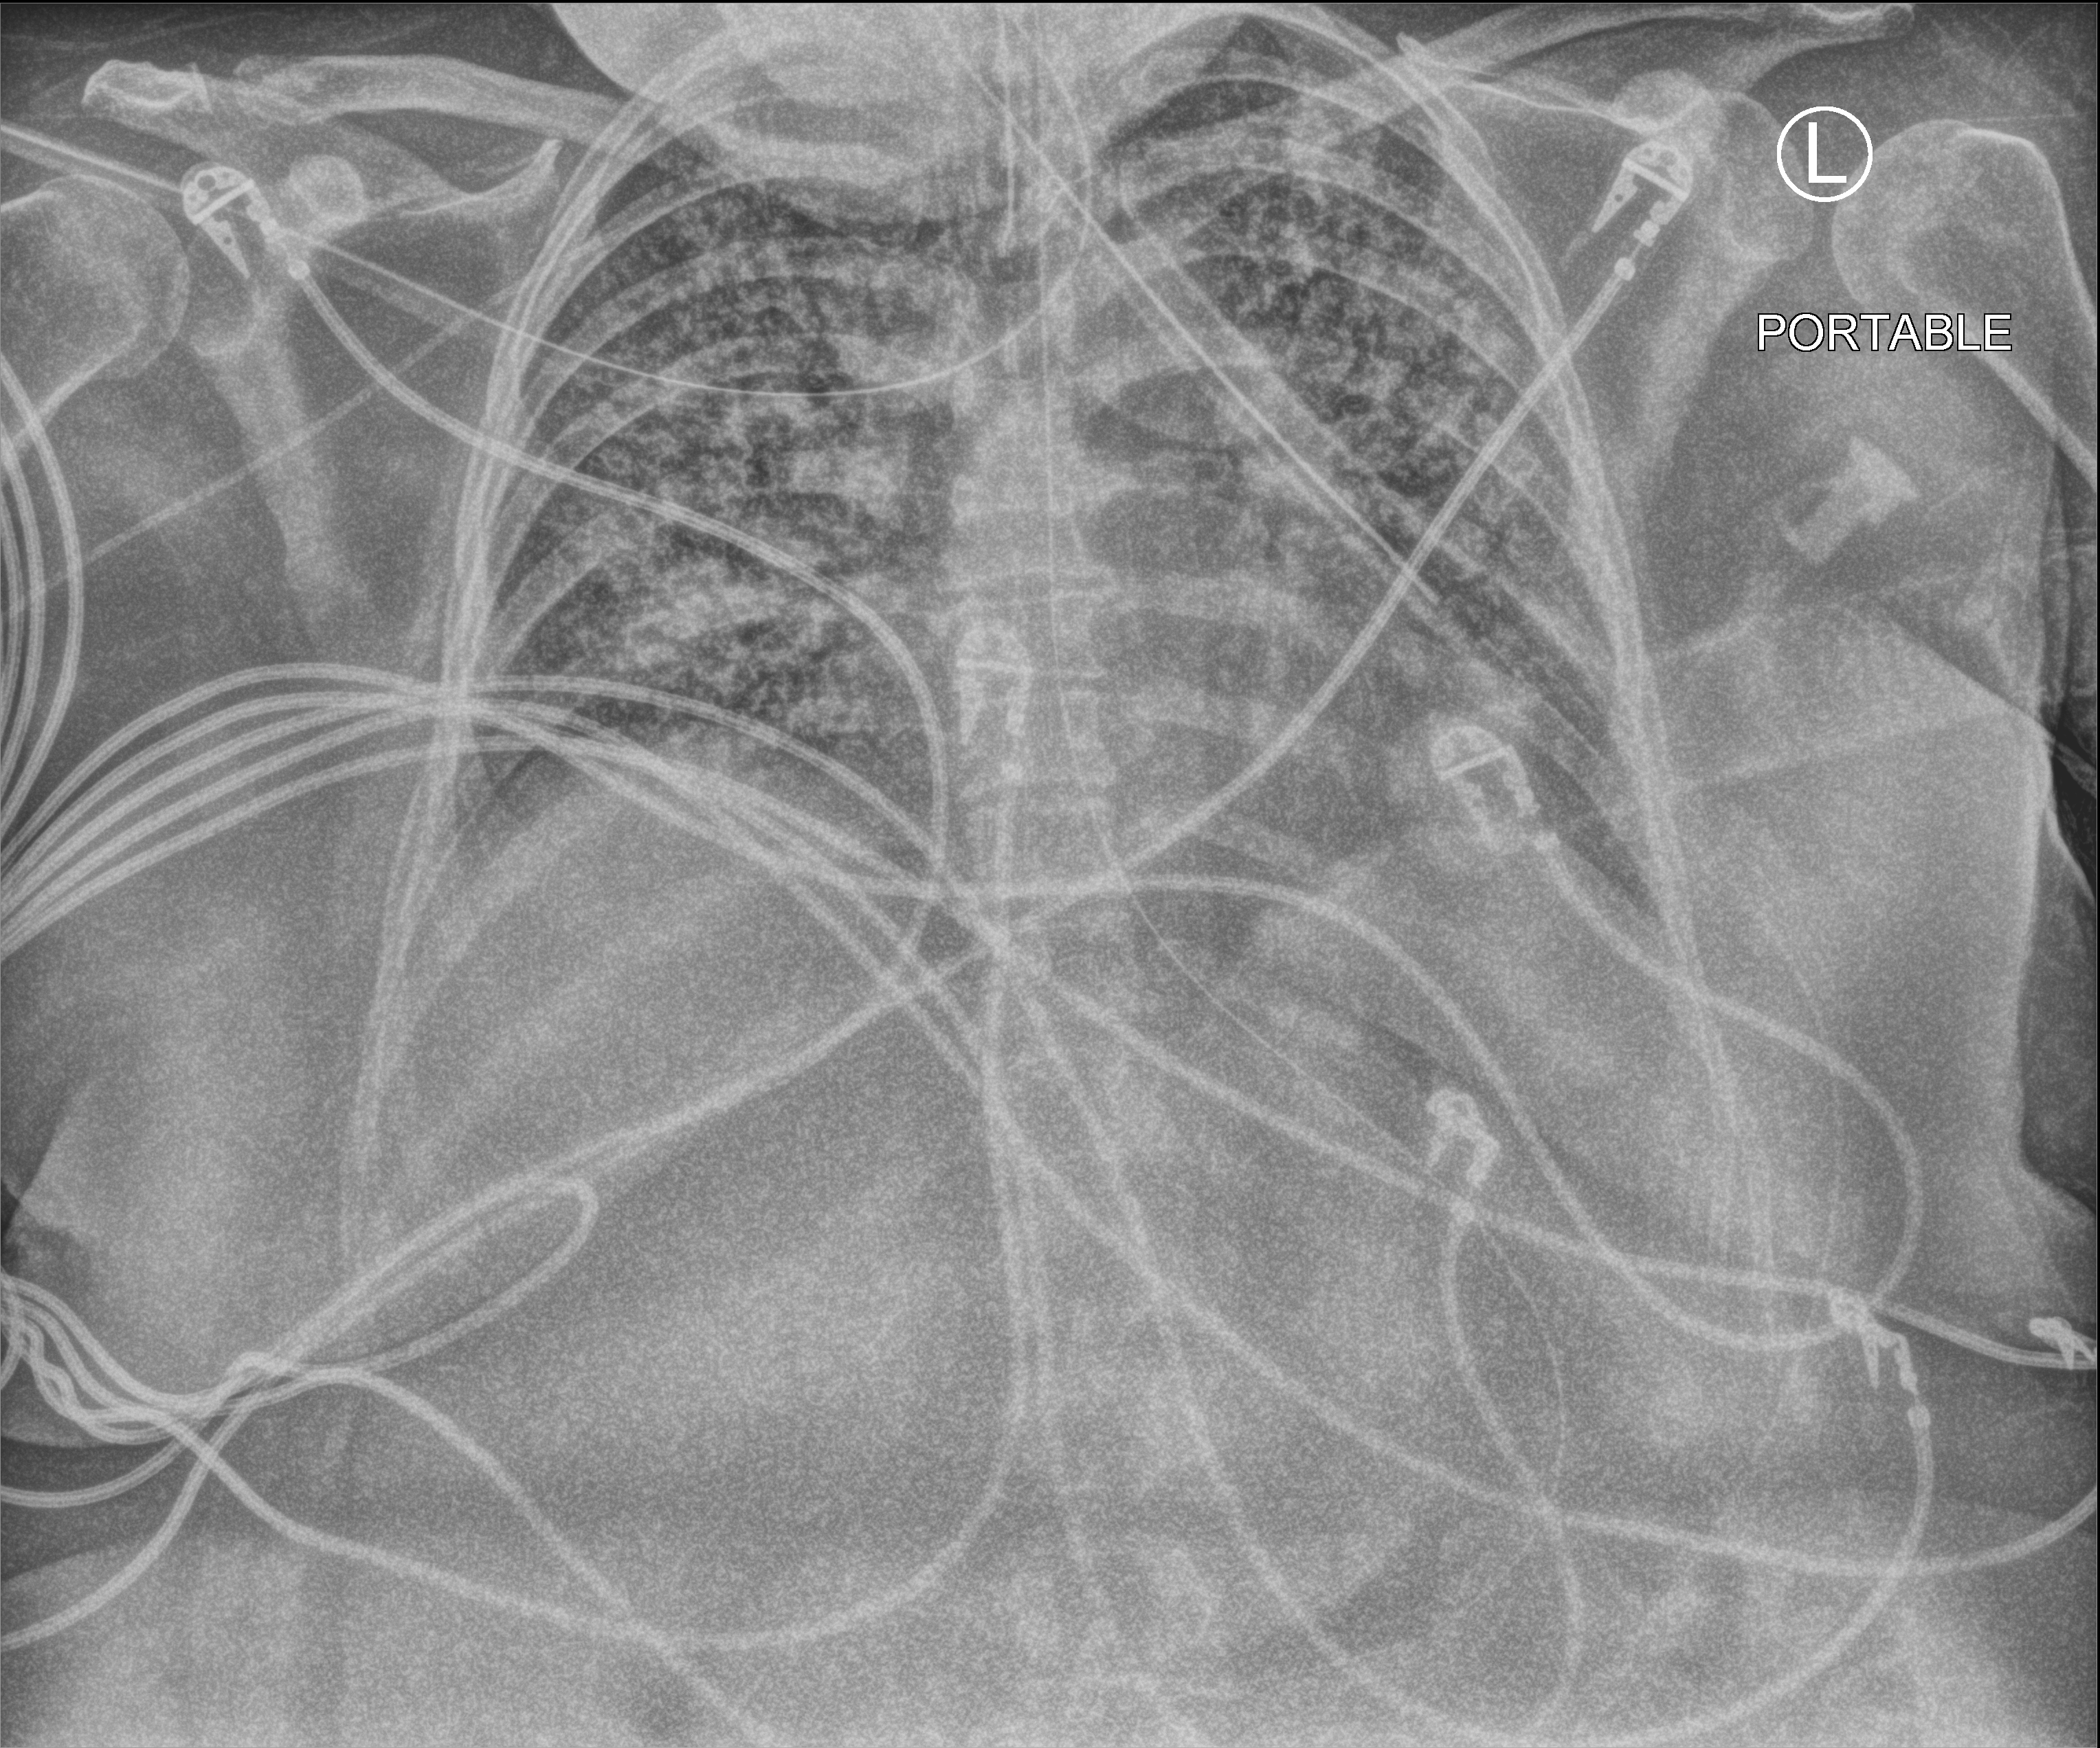
Chest X-ray (portable); anteroposterior (AP) projection. Patient hospitalised with COVID-19; female, aged 18–59 years.
From the hospital-stay record, not from the radiograph (when in the stay this image was taken is not recorded): mechanically ventilated during this hospital stay: yes; COPD (admission record): no; length of hospital stay: 95 days.